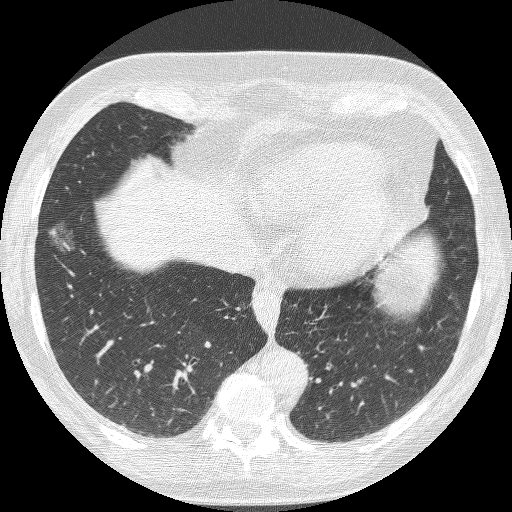
Chest CT (low-dose screening protocol), one axial image; baseline screening round; lung window (W 1500 / L -600 HU); lung (sharp) reconstruction kernel (BONE); slice 69 of 221 in the series. Female participant, aged 68 years at enrolment. Current smoker at enrolment.
Expert-annotated lung lesion, bounding box <34,221,86,272> (left, top, right, bottom; pixels). Reader record for this screening exam (exam-level; its link to the box is not recorded): non-calcified nodule or mass ≥4 mm, right lower lobe, 16 × 12 mm, poorly defined margins, ground glass attenuation. Lung cancer was diagnosed 406 days after this screen (after the second annual screen): bronchiolo-alveolar adenocarcinoma, NOS, right lower lobe, well differentiated (G1), stage IA (AJCC 6th edition), 13 mm at pathology.